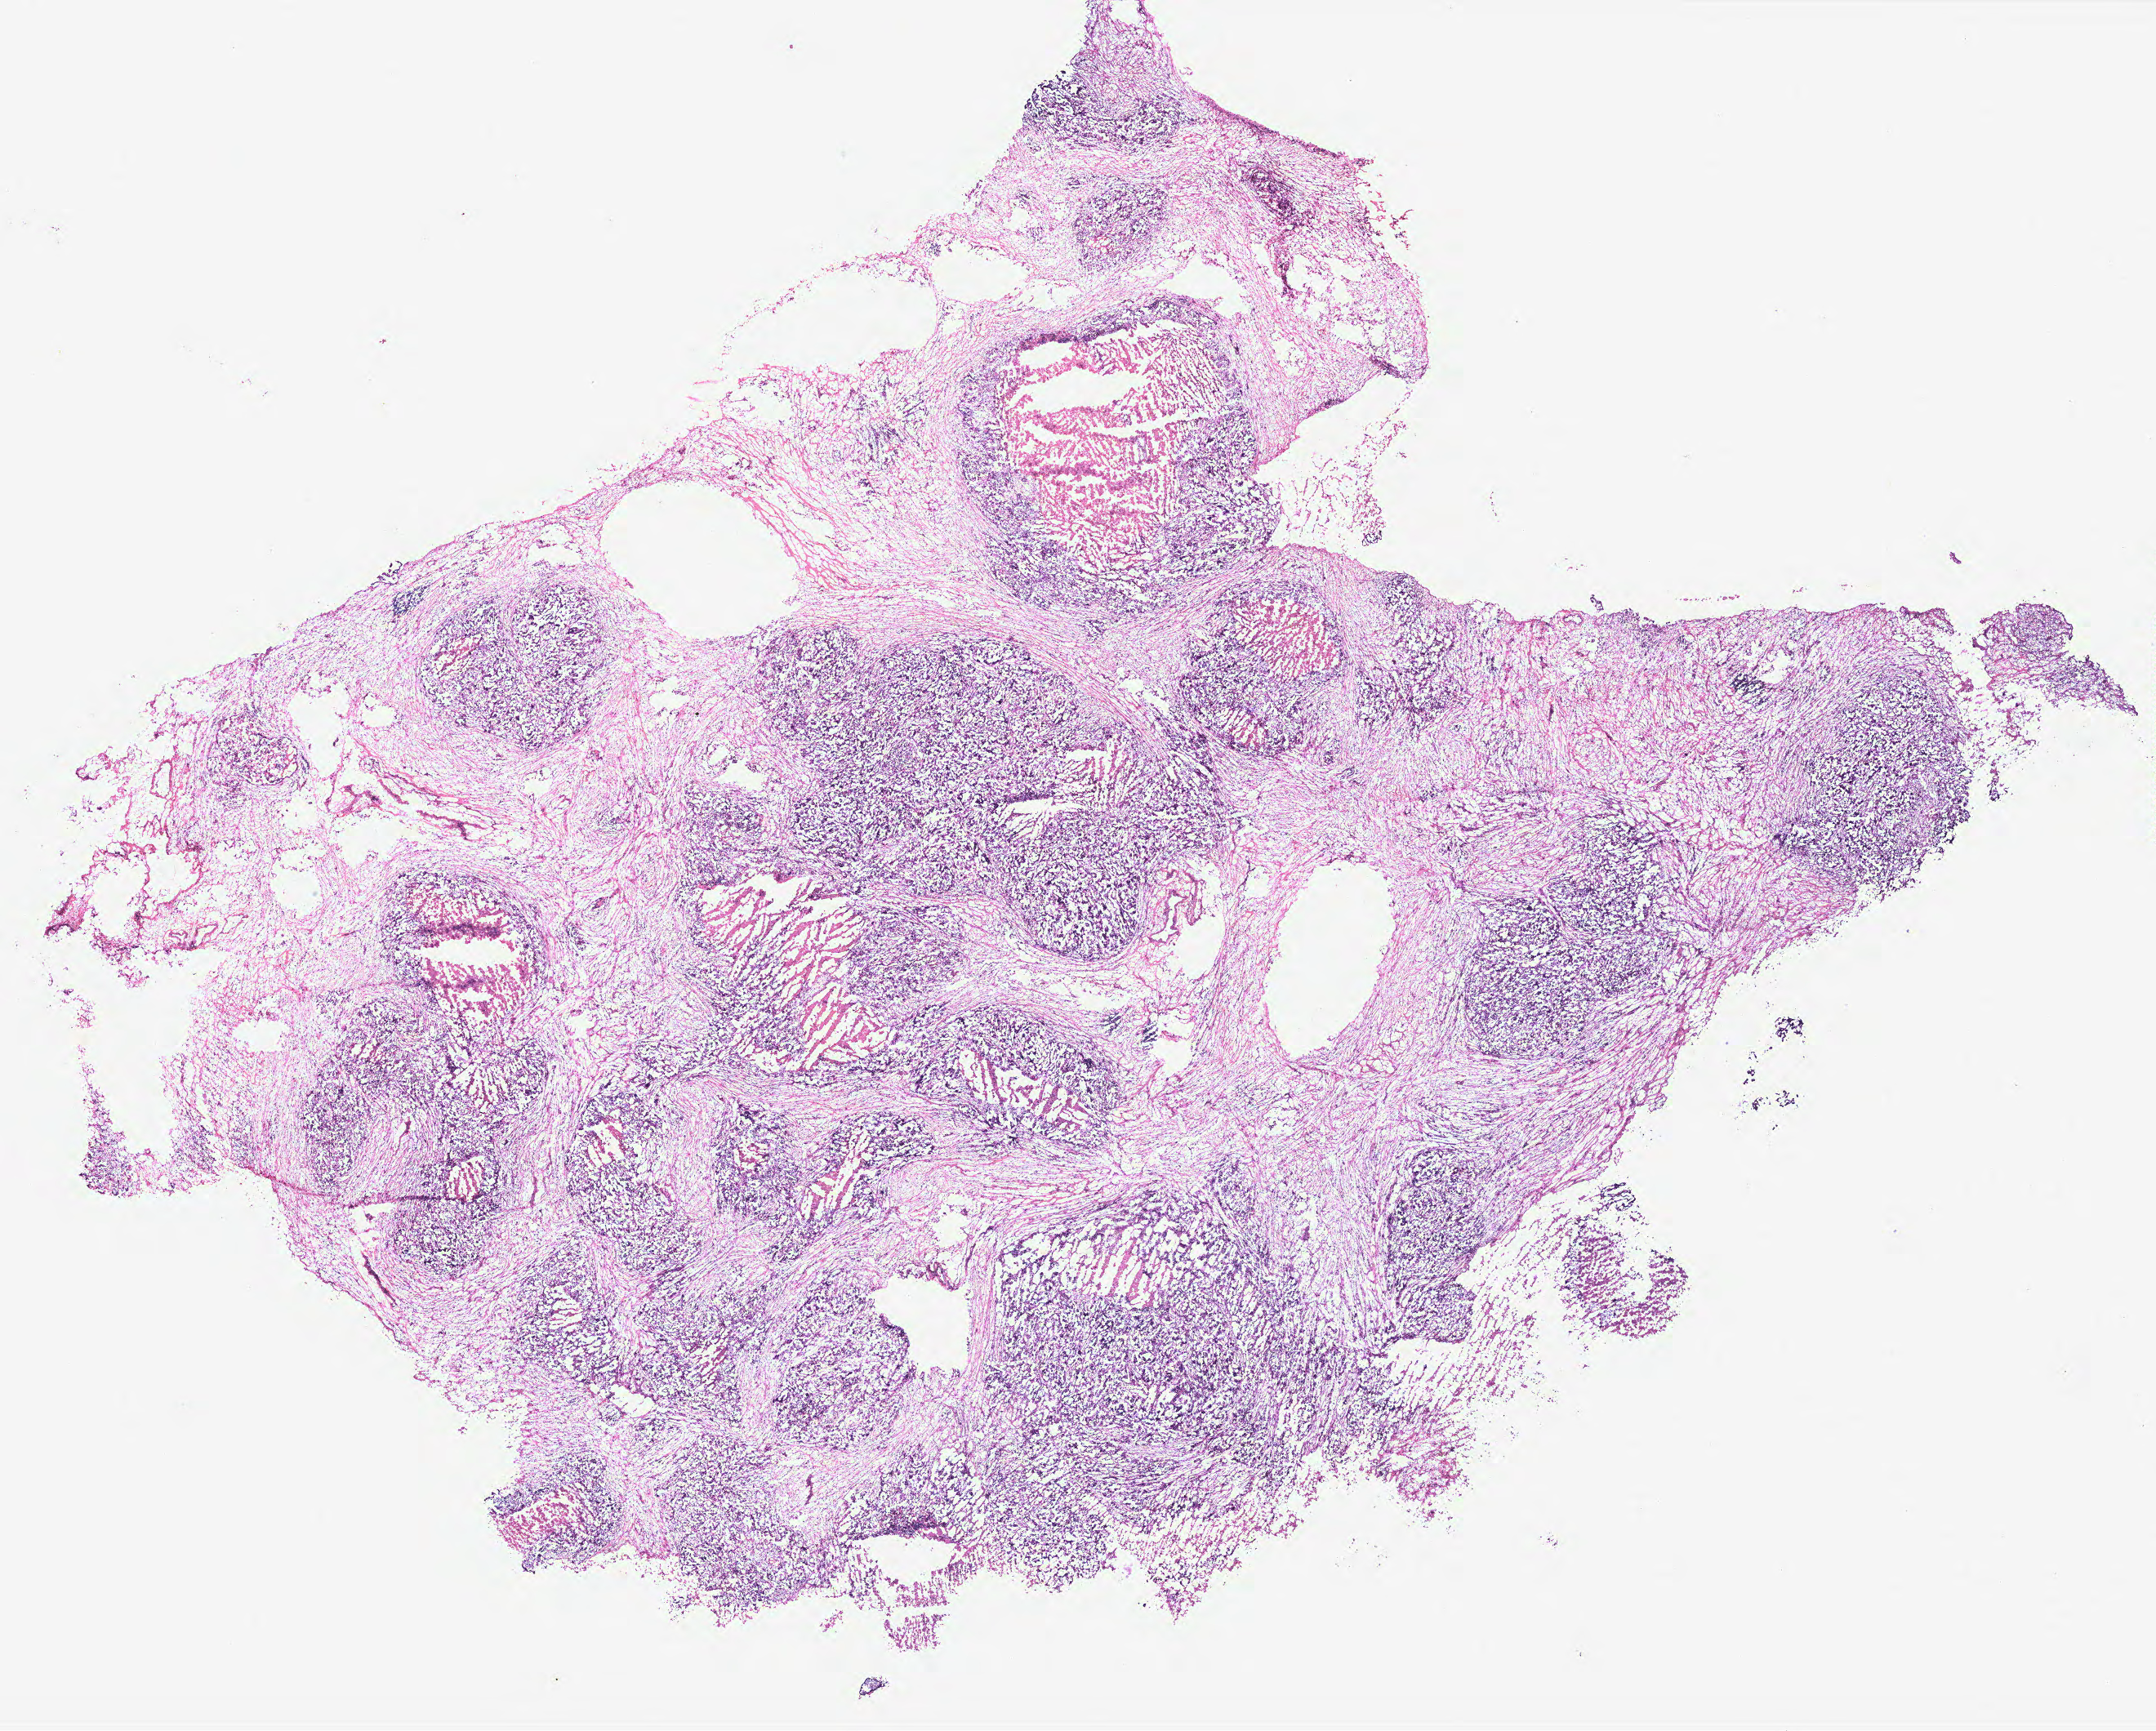
Whole-slide histology image, Hematoxylin and eosin (H&E) stained — shown as a low-resolution overview of the whole scanned area (about 21.1 x 17.0 mm); tumour tissue sample, ovary. Female, 66 y/o.
Diagnosis: Serous adenocarcinoma, NOS.